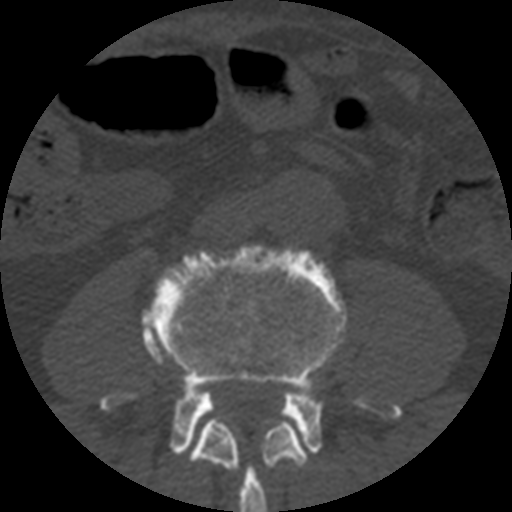
CT including the spine, one axial slice. Slice 102 of 508 in the series (ordered by position). Reconstruction kernel STANDARD. 120 kVp. Bone window (W 1800 / L 400 HU). 512 × 512 image matrix. Patient age 57 years. From the clinical record (not read from this slice): primary cancer: prostate.
Structures marked on this image (semi-automatic segmentation, software-assisted and operator-edited):
- L3 vertebra: box from (x=190, y=419) to (x=307, y=512) px
- L4 vertebra: (x=101, y=244)–(x=402, y=458)